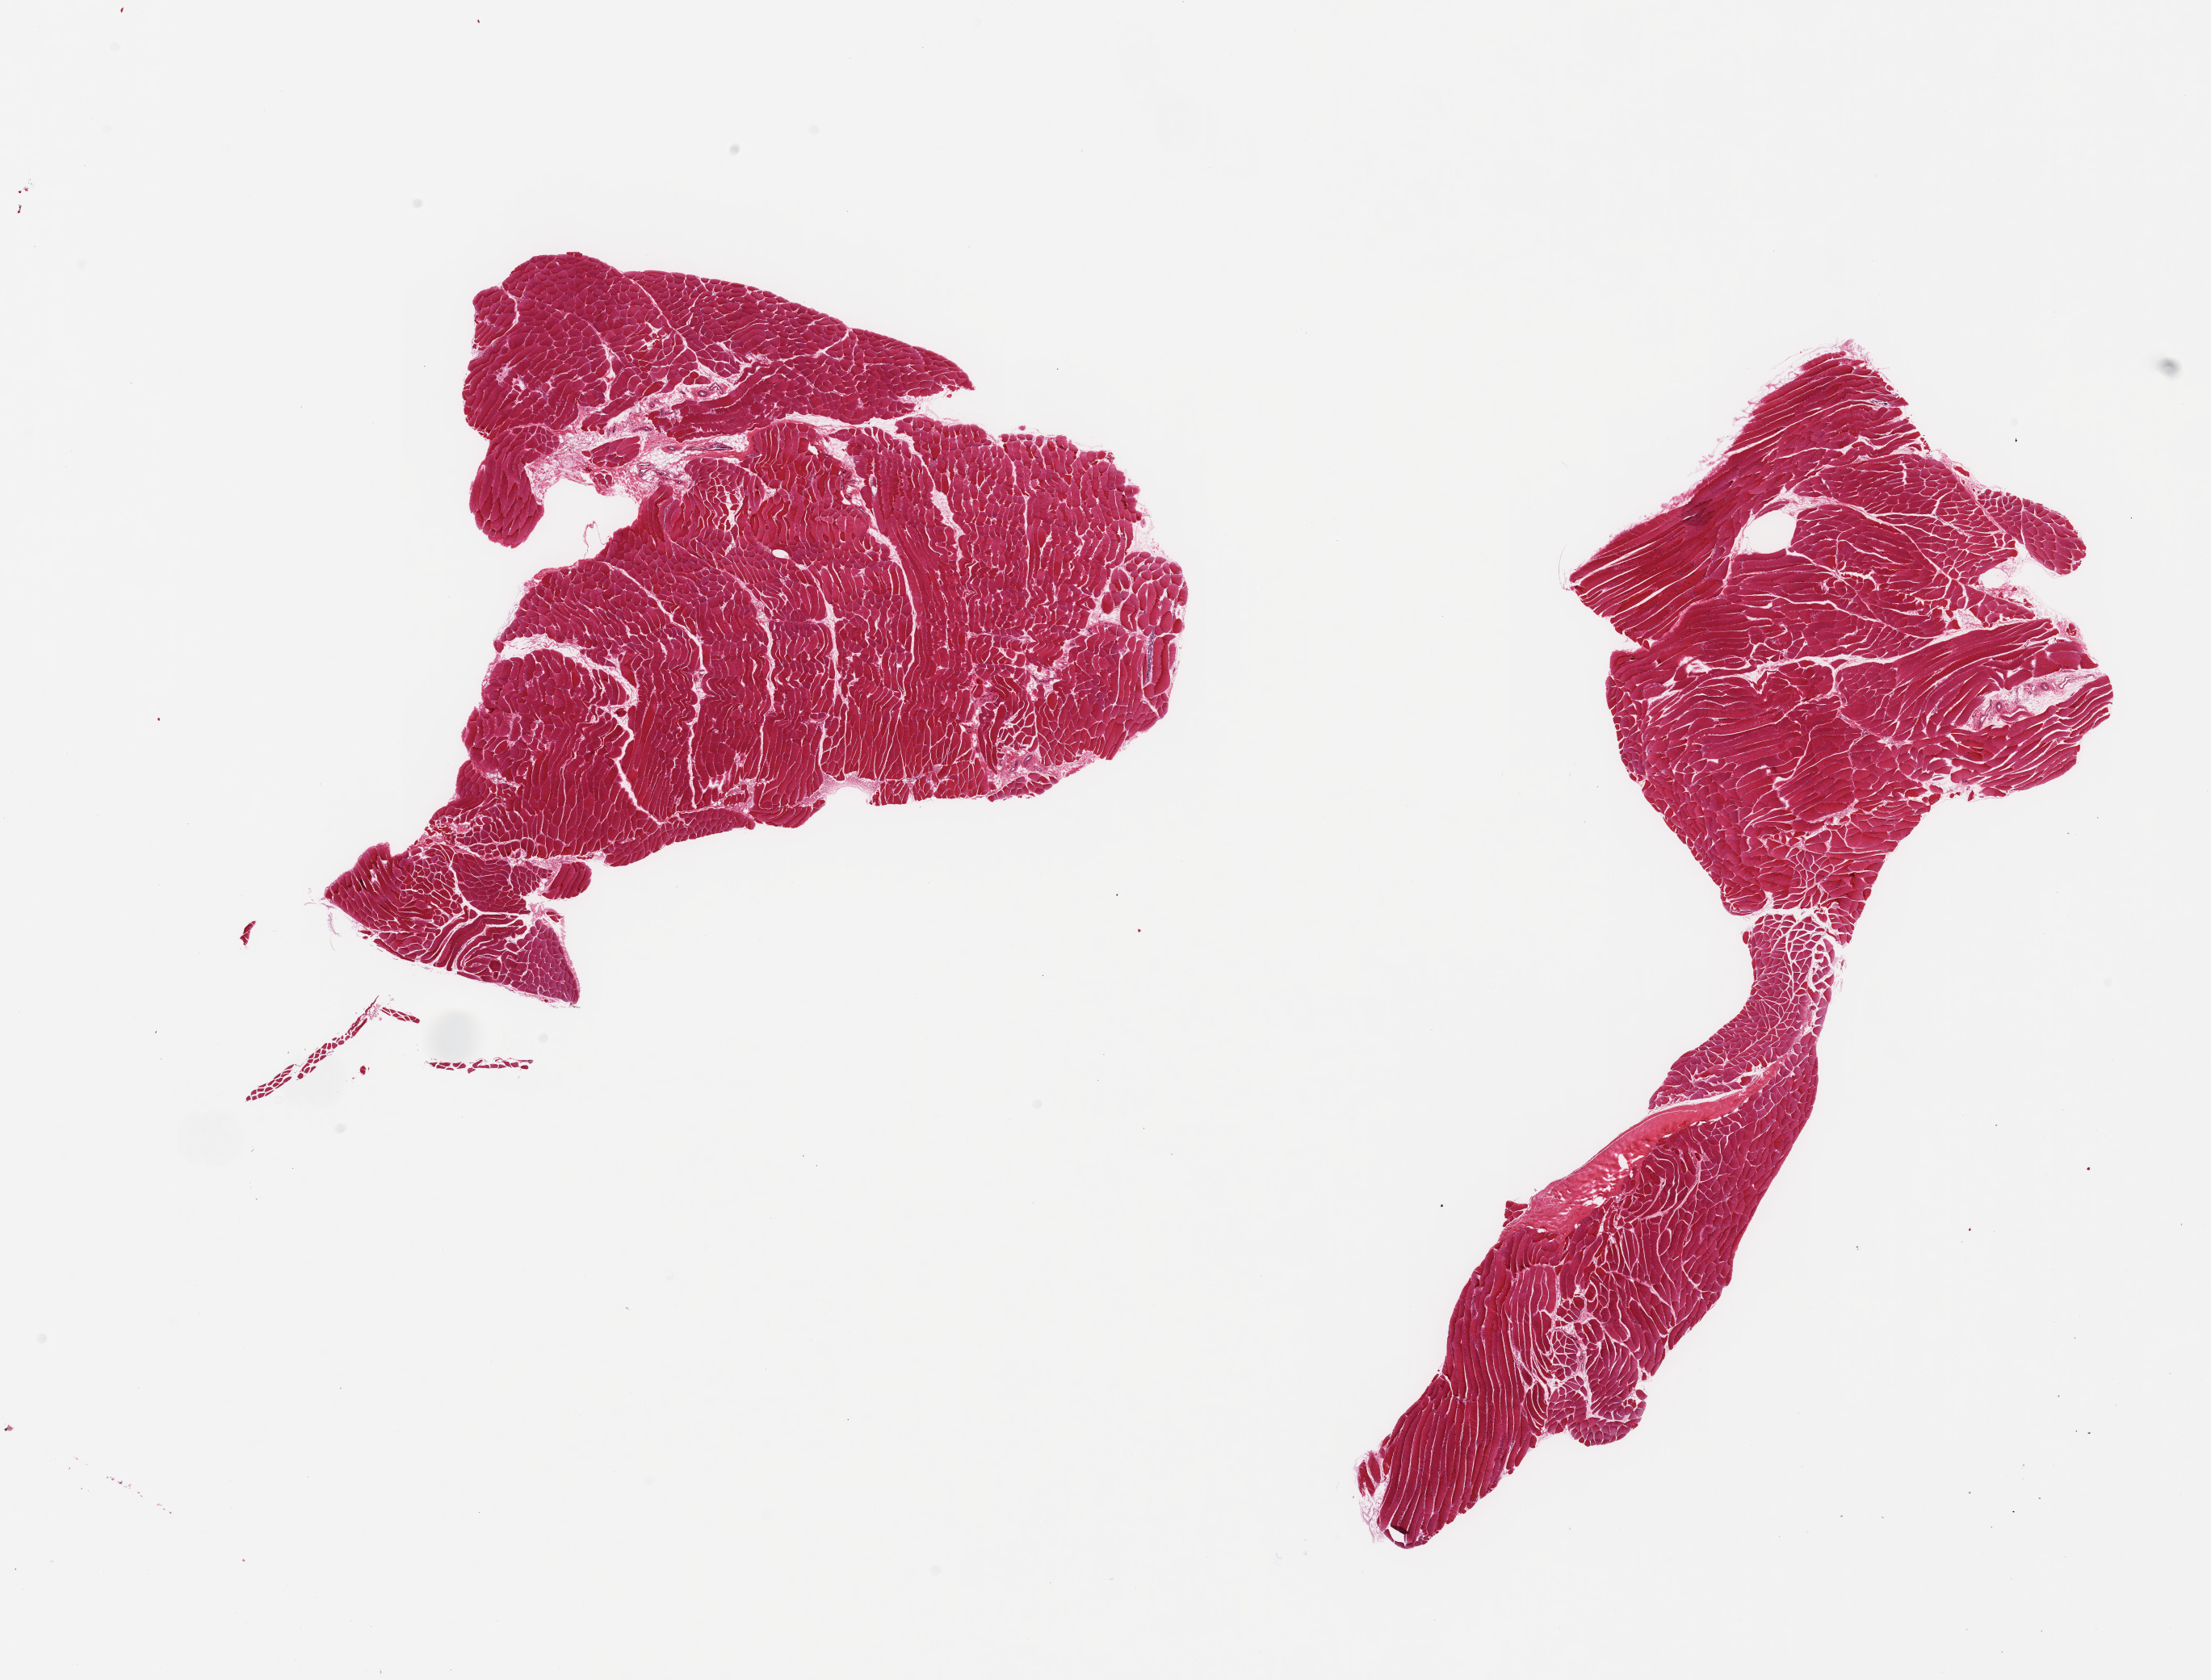
H&E whole-slide image — whole scanned area (about 21.7 x 16.5 mm, acquisition: 20x scan) shown as a low-resolution overview. PAXgene-fixed, paraffin-embedded tissue. Sampled site (target tissue): skeletal muscle. Tissue donor sample.
- pathologist's review note for this sample: 2 pieces; sliver of tendon in 1 piece, 2% of area